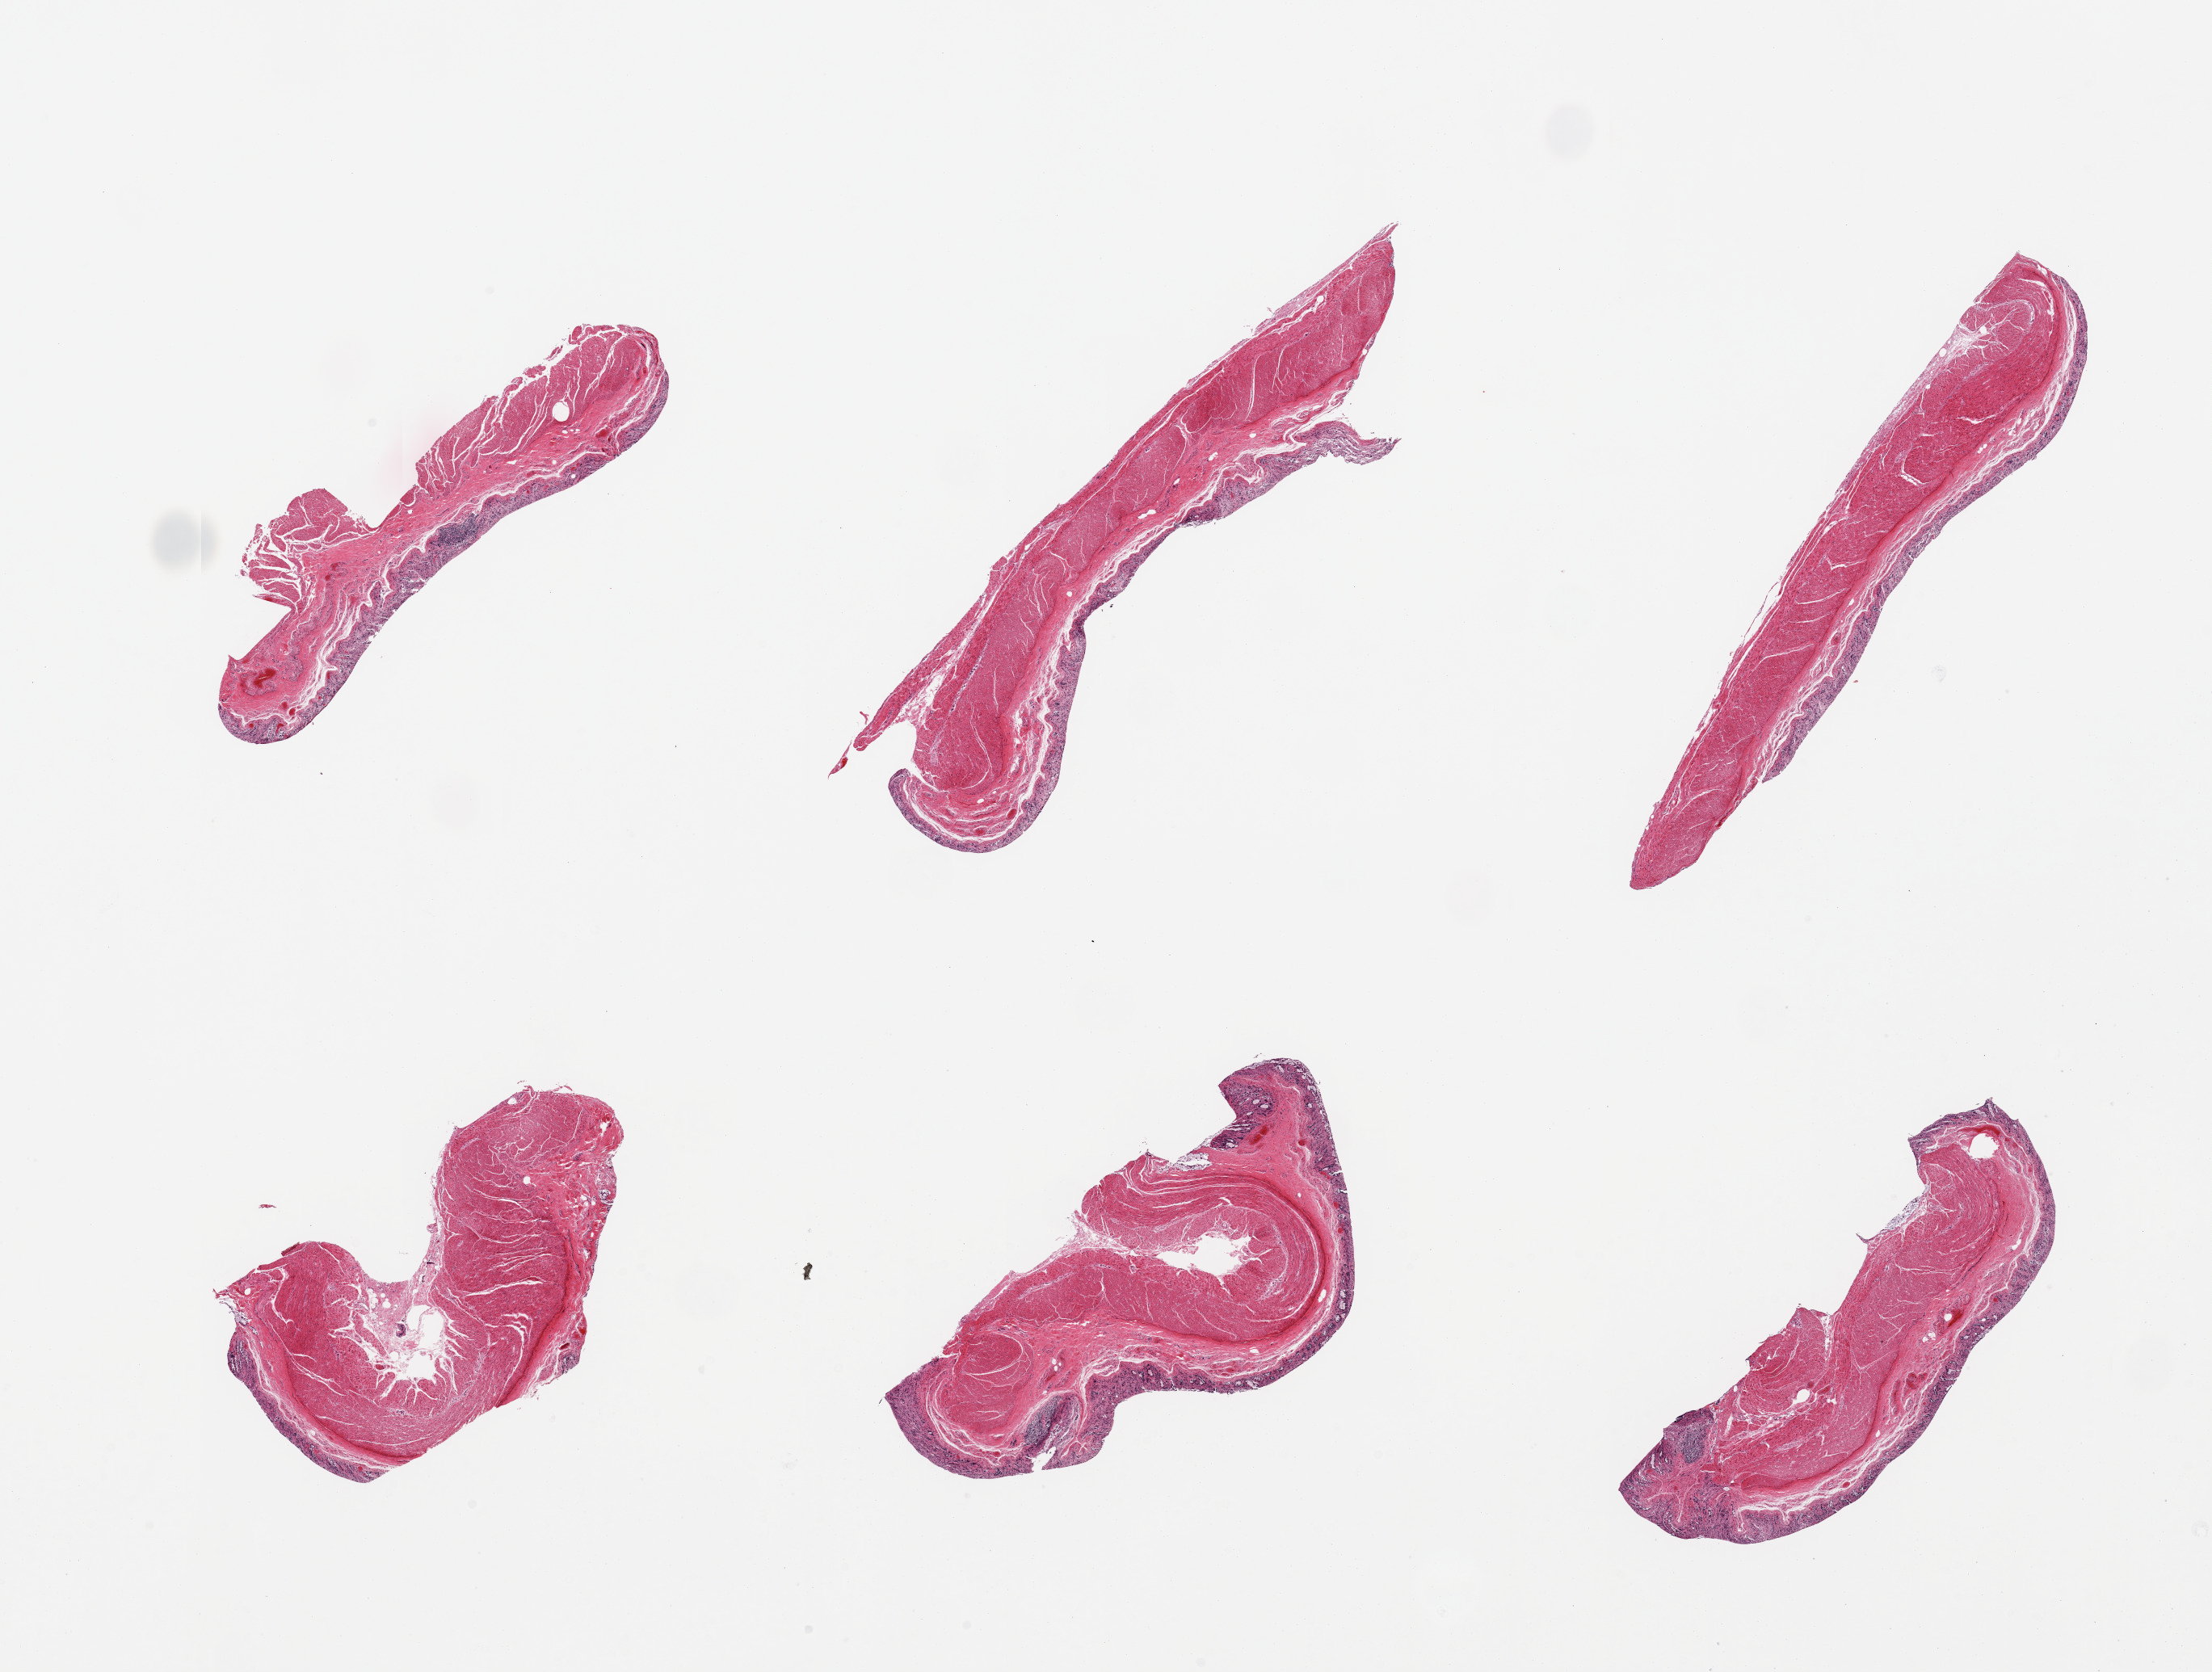
Digitized H&E-stained section, brightfield — a low-resolution overview of the entire scanned area, about 21.7 x 16.4 mm. Donor: female.
- specimen: PAXgene-fixed paraffin-embedded (PFPE) section; target tissue: transverse colon; donor tissue sample